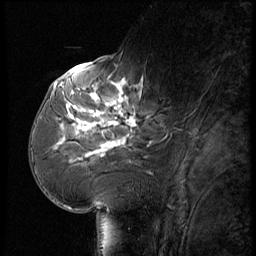
Breast MRI (dynamic contrast-enhanced), one sagittal slice. Dynamic contrast-enhanced series, image 2 of 3 at this slice position (ordered by acquisition). 1.5 T. TE 4.2 ms, TR 9 ms. 2.5 mm slice thickness. 256 × 256 image matrix, field of view 180 × 180 mm. Female patient, age 61 years. Case-level facts recorded for this patient, not image findings: setting: breast cancer imaged before/during neoadjuvant chemotherapy; receptor status: HR-positive, HER2-negative.
Structures marked on this image (semi-automatic segmentation, software-assisted and operator-edited):
- analysis volume of interest (the breast-tissue region the enhancement analysis was run in; not a lesion): box from (x=65, y=74) to (x=178, y=175) px
- tumour enhancement mask (voxels above the 140 % enhancement threshold inside the analysis volume of interest): (x=70, y=78)–(x=144, y=161)